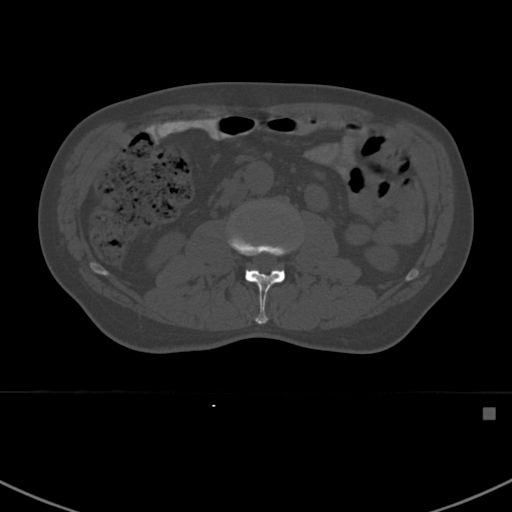
CT including the spine, one axial slice. Position 280 of 412 along the scan axis. 120 kVp. Bone window (W 1800 / L 400 HU). 1.5 mm slice thickness. 512 × 512 image matrix, field of view 358 × 358 mm. Patient: male, 59 years. Case-level facts recorded for this patient, not image findings: primary cancer: prostate.
Outlined on this slice (semi-automatically segmented with operator editing):
- L2 vertebra: box from (x=228, y=229) to (x=297, y=324) px
- L3 vertebra: (x=272, y=203)–(x=286, y=211)